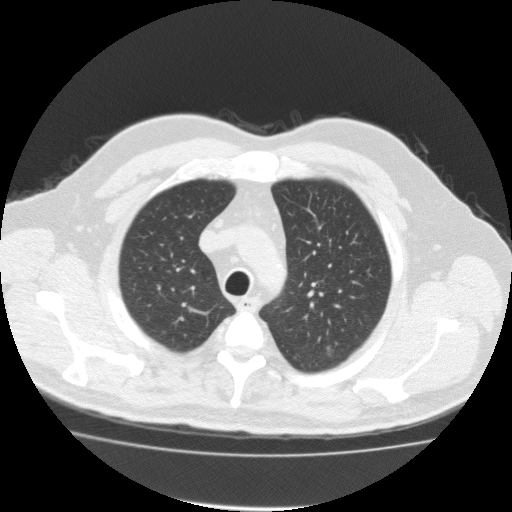
Chest CT (low-dose screening protocol), one axial image, first (baseline) screen, lung window (W 1500 / L -600 HU), 120 kVp, slice 29 of 161 in the series. Male participant, aged 57 years at enrolment.
Expert-annotated lung lesion, bounding box (x1, y1, x2, y2) in pixels: (317, 335, 353, 373). Reader record for this screening exam (exam-level; its link to the box is not recorded): non-calcified nodule or mass ≥4 mm, left upper lobe, 11 × 8 mm, spiculated (stellate) margins, soft tissue attenuation. Participant outcome: lung cancer diagnosed 19 days after this screen — bronchiolo-alveolar adenocarcinoma, NOS, left upper lobe, well differentiated (G1), stage IA (AJCC 6th edition), 80 mm at pathology.